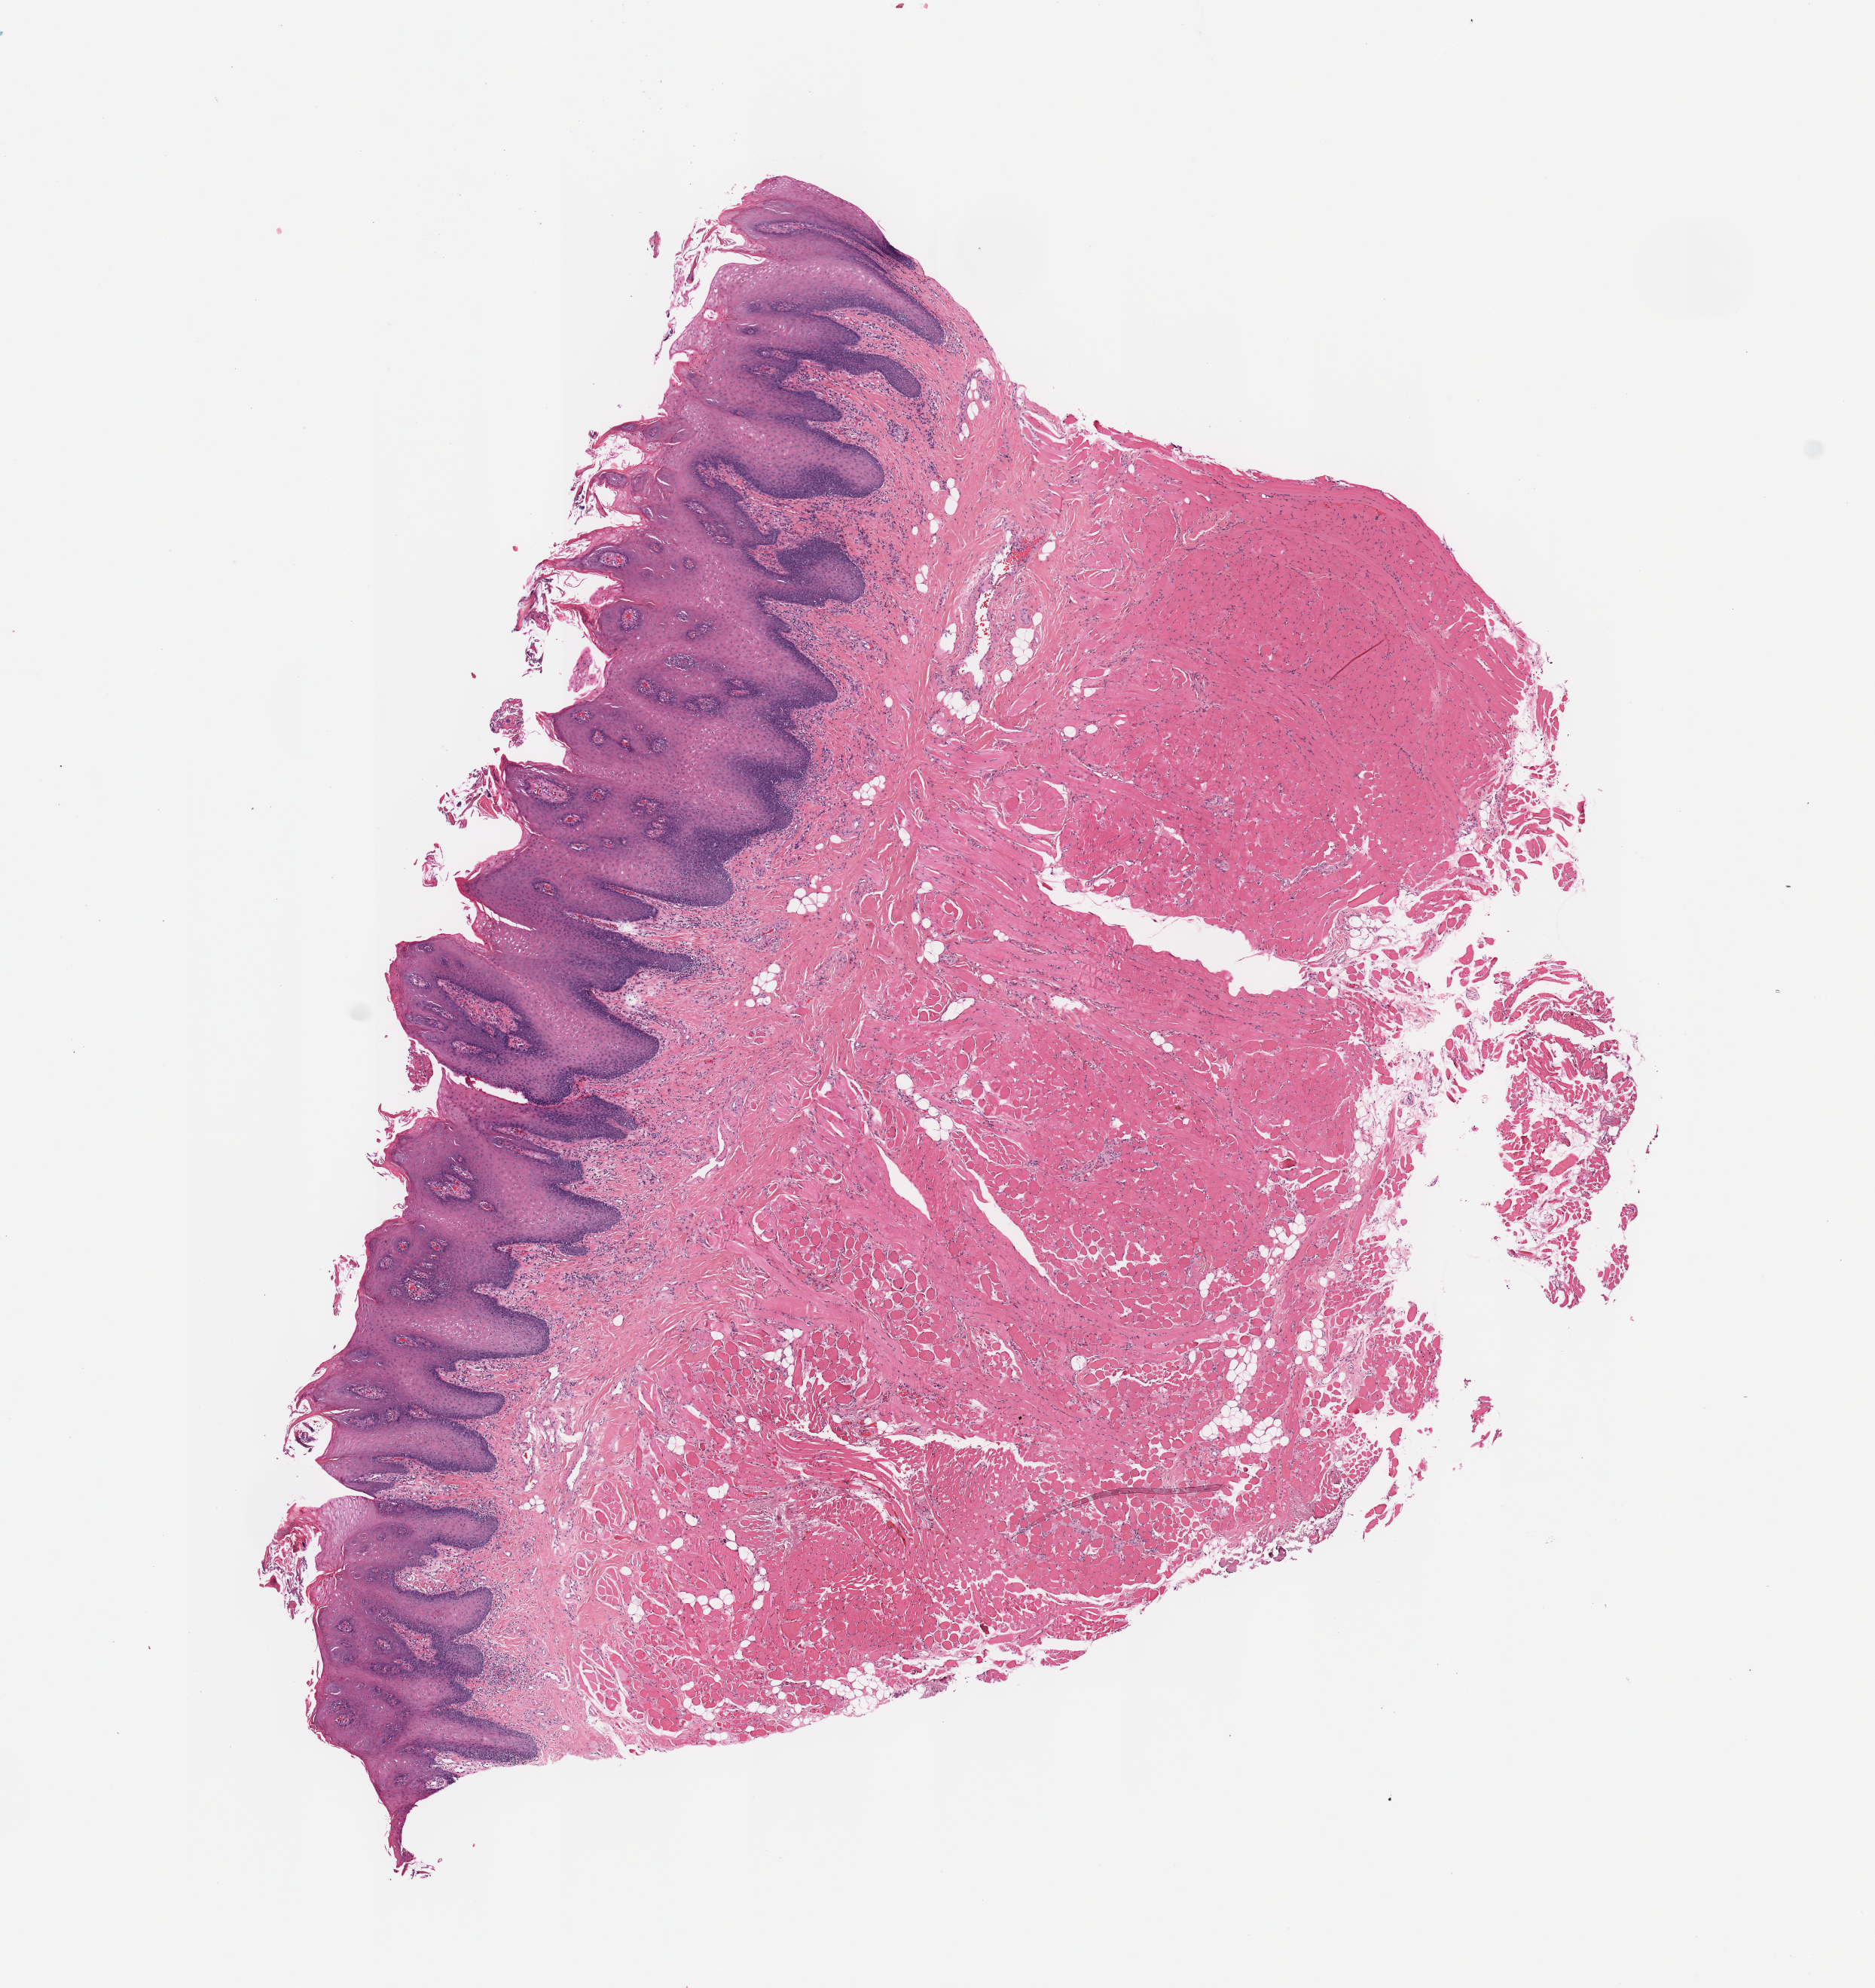
Whole-slide histology image, Hematoxylin and eosin (H&E) stained — a low-resolution overview of the entire scanned area, about 9.8 x 10.4 mm (from a 20x scan); normal (non-tumour) tissue sample, sampled site: oral cavity. Male, 54 y/o.
* this section: normal (non-tumour) tissue from the same patient
* patient diagnosis: Squamous cell carcinoma, NOS (overlapping lesion of lip, oral cavity and pharynx)